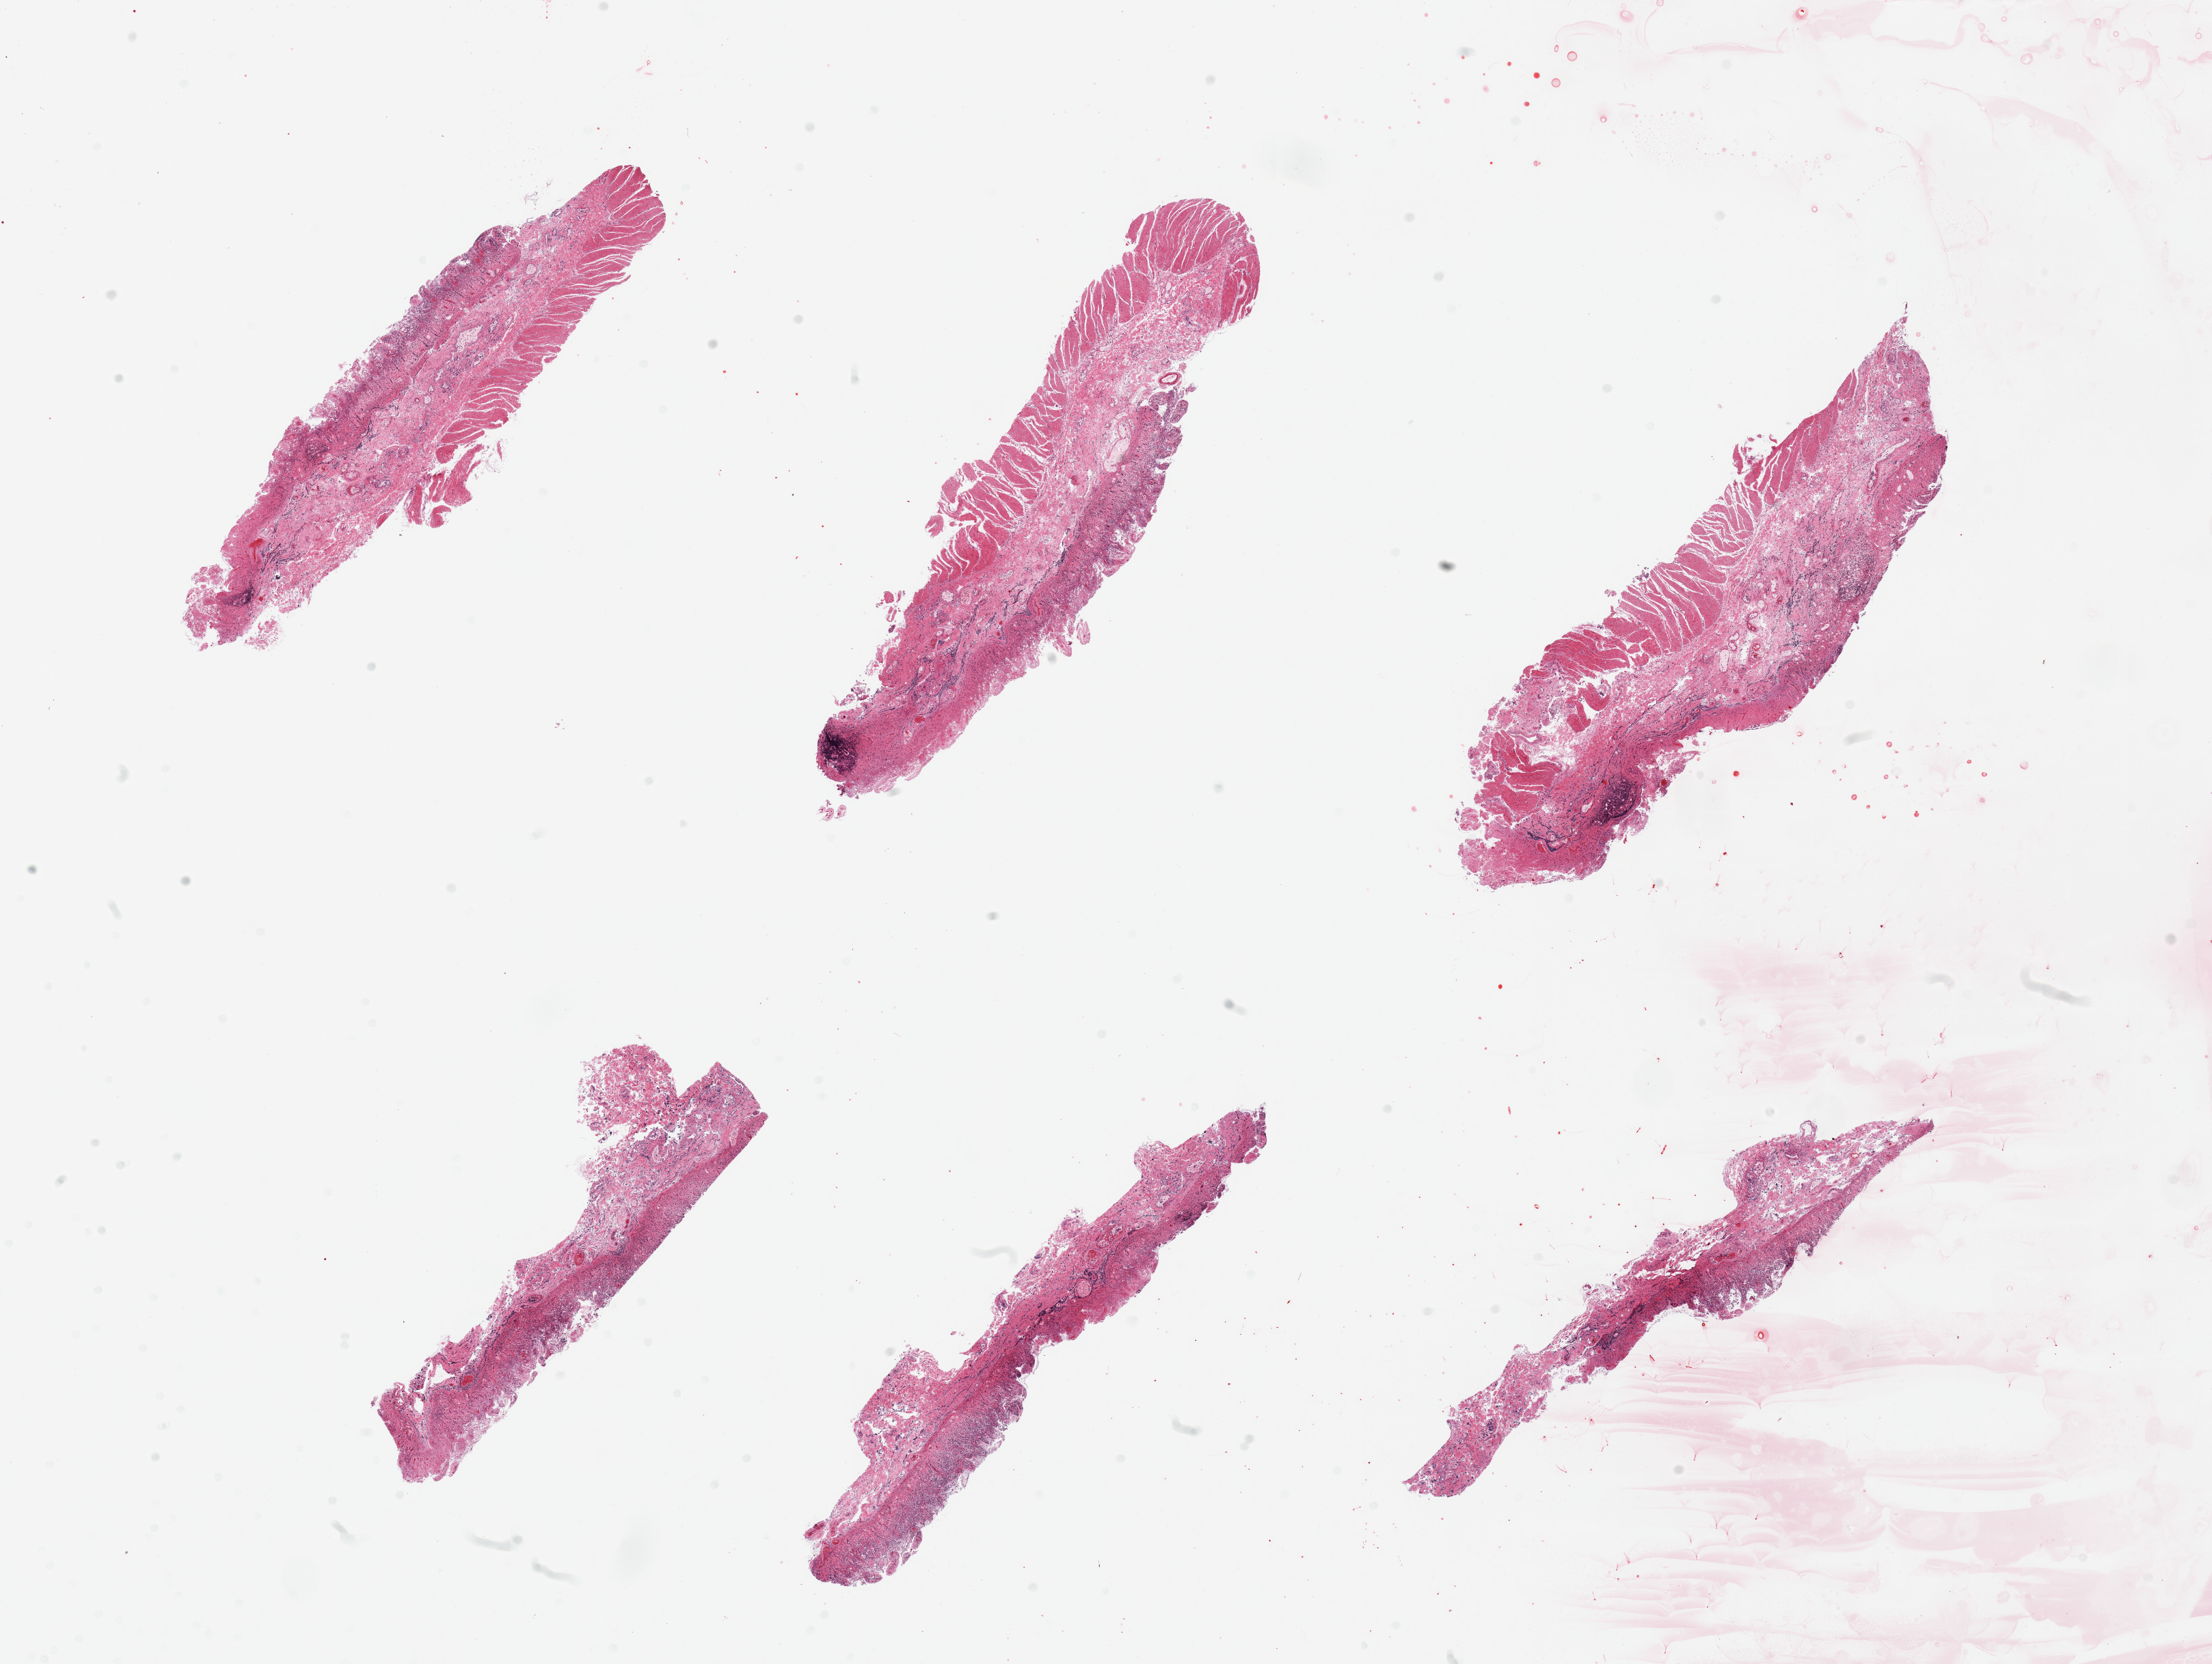
Whole-slide image, haematoxylin and eosin stain — whole scanned area (about 25.6 x 19.3 mm) shown as a low-resolution overview; PAXgene-fixed, paraffin-embedded tissue; target tissue: ileum; tissue donor sample. Donor sex: male.
Review note (as recorded): 4 pieces, no viable mucosa.